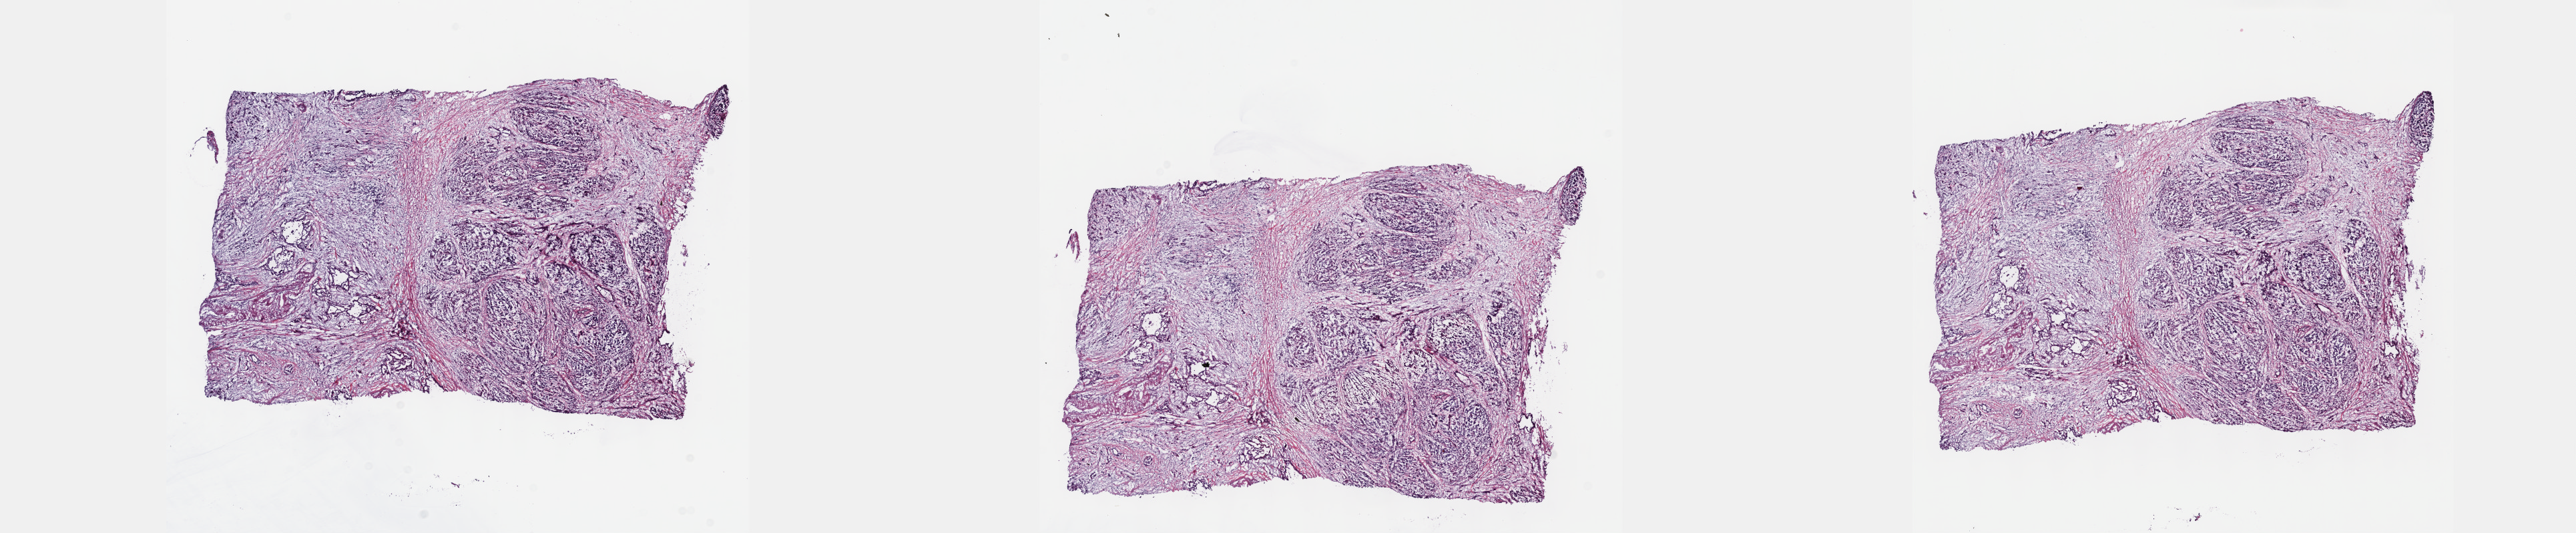
H&E-stained whole-slide image, shown as a low-resolution overview of the whole scanned area (about 31.2 x 6.4 mm); frozen section from the top of the tissue portion; pancreas, primary tumour sample. Female patient; age at initial diagnosis 70 years. Histologic grade: G1 (well differentiated). Composition of this section per pathologist review: tumour cells 70%, tumour nuclei 70%, normal cells 0%, stromal cells 30%, necrosis 0%. Inflammatory infiltration, as recorded: lymphocyte infiltration 40%, monocyte infiltration 20%, neutrophil infiltration 20%.
* pathologic diagnosis: Infiltrating duct carcinoma, NOS (head of pancreas)
* AJCC pathologic stage: IIB (7th edition)